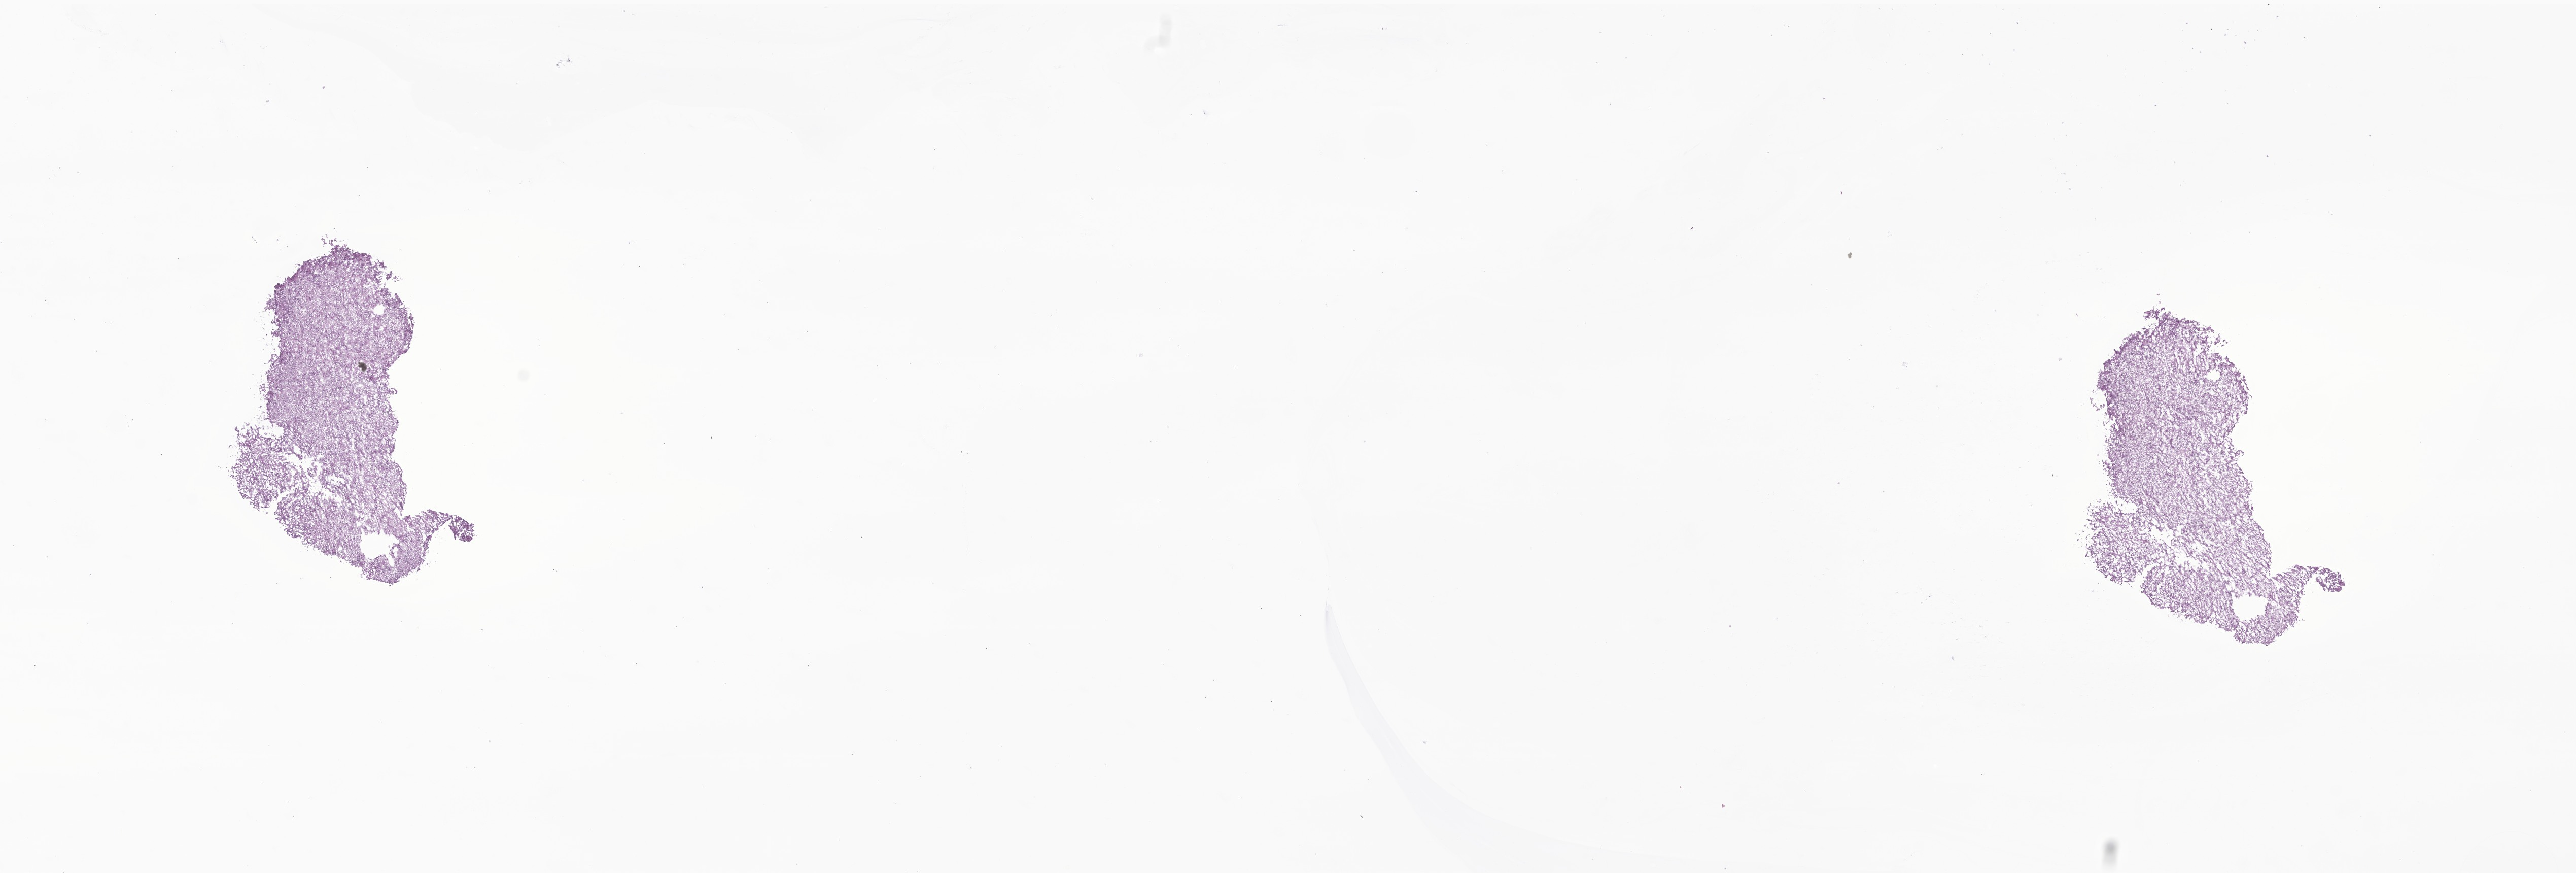
Whole-slide image, haematoxylin and eosin stain of tumor tissue from the brain, a low-resolution overview of the entire scanned area, about 21.4 x 7.3 mm; cryosection (OCT / tissue freezing medium). Patient: male, age 256 months (21 years 4 months).
Recorded diagnosis: Meningioma, NOS.